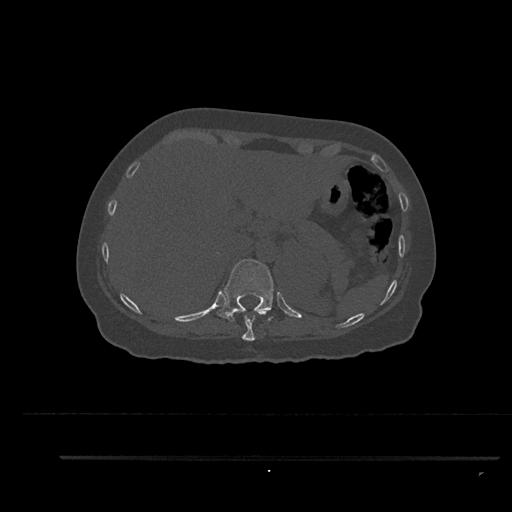
CT including the spine, one axial slice; position 332 of 797 along the scan axis; reconstruction kernel Br40s/3; 120 kVp; bone window (W 1800 / L 400 HU); 0.5 mm slice thickness; 512 × 512 image matrix, field of view 408 × 408 mm. Female patient, age 44 years. Case-level facts recorded for this patient, not image findings: primary cancer: renal.
Structures marked on this image (semi-automatic segmentation, software-assisted and operator-edited):
- T10 vertebra: bounding box (x1, y1, x2, y2) in pixels: (242, 308, 255, 341)
- T11 vertebra: (216, 259, 274, 322)